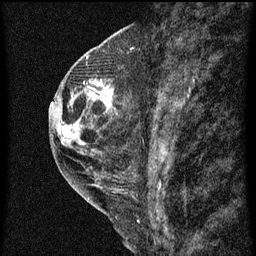
Breast MRI (dynamic contrast-enhanced), one sagittal slice. Position 24 of 60 along the scan axis. Dynamic contrast-enhanced series, image 2 of 3 at this slice position (ordered by acquisition). 1.5 T. TE 4.2 ms, TR 8 ms. 2 mm slice thickness. 256 × 256 image matrix, field of view 180 × 180 mm. Female patient, age 48 years.
Annotated regions visible in this slice (semi-automatically segmented with operator editing):
- analysis volume of interest (the breast-tissue region the enhancement analysis was run in; not a lesion): bounding box (x1, y1, x2, y2) in pixels: (89, 72, 118, 113)
- tumour enhancement mask (voxels above the 70 % enhancement threshold inside the analysis volume of interest): (94, 80, 115, 105)